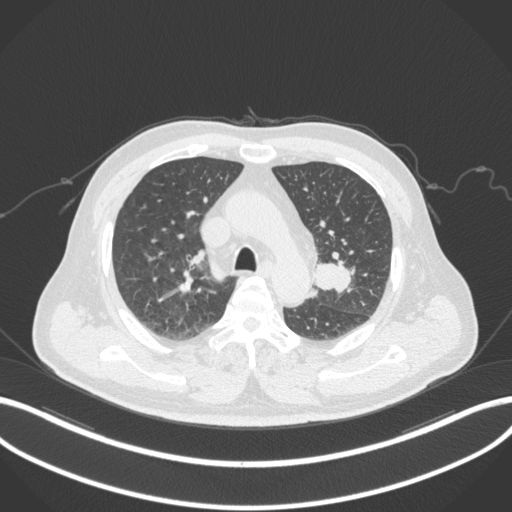
Chest CT, one axial slice. Position 209 of 286 along the scan axis. Reconstruction kernel B31f. 120 kVp. Lung window (W 1500 / L -600 HU). 512 × 512 image matrix, field of view 400 × 400 mm. Male patient, age 67 years. Case-level facts recorded for this patient, not image findings: clinical TNM (as recorded): T2a N1 M0.
Structures marked on this image (rectangle marked by the reading radiologist):
- lung tumour (recorded histology: adenocarcinoma): box from (x=313, y=261) to (x=354, y=294) px